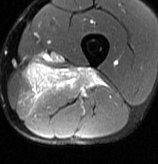
MRI of an extremity soft-tissue mass, one axial slice; slice 26 of 70 in the series (ordered by position); T2-weighted fat-saturated; MR volume resampled by the dataset authors to the PET/CT grid (not the native acquisition matrix); 3.27 mm slice thickness; 158 × 164 image matrix, field of view 154 × 160 mm. Male patient. Case-level facts recorded for this patient, not image findings: histological type: extraskeletal osteosarcoma; grade: high; site of the primary tumour: left adductur.
Structures marked on this image (expert contour drawn on MRI and transferred to this co-registered scan by the dataset authors):
- gross tumour volume (mass): bounding box <24,62,105,99> (left, top, right, bottom; pixels)